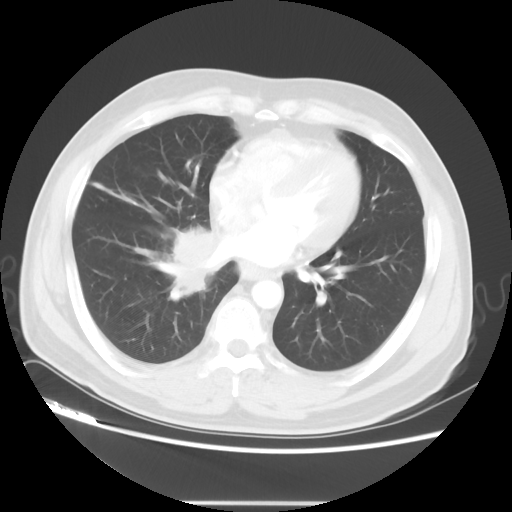
Chest CT, one axial slice. Slice 18 of 48 in the series (ordered by position). Lung window (W 1500 / L -600 HU). 5 mm slice thickness. 512 × 512 image matrix. Patient: male, 53 years. Case-level facts recorded for this patient, not image findings: clinical TNM (as recorded): T2 N3 M0; histopathological grade: G3.
Outlined on this slice (rectangle marked by the reading radiologist):
- lung tumour (recorded histology: small cell carcinoma): bounding box <155,227,219,298> (left, top, right, bottom; pixels)